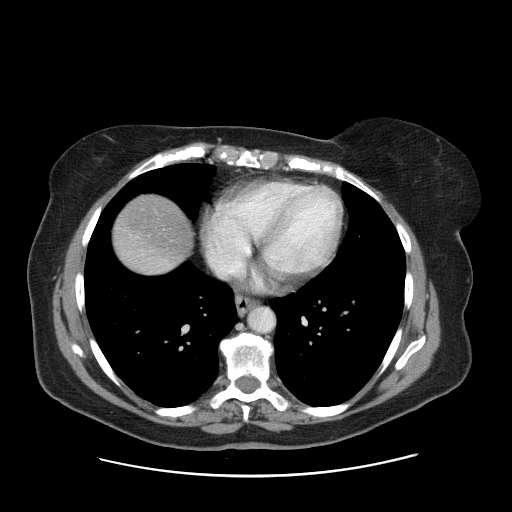
Contrast-enhanced abdominal CT, one axial slice; position 150 of 161 along the scan axis; soft-tissue window (W 400 / L 40 HU); 2.5 mm slice thickness; 512 × 512 image matrix, field of view 398 × 398 mm. Female patient, age 62 years. From the clinical record (not read from this slice): diagnosis: colorectal cancer liver metastases, imaged before liver resection; multiple liver metastases: no; largest metastasis: 2.5 cm; disease in both lobes: no.
Annotated regions visible in this slice (manually delineated by an expert):
- liver: bounding box [x1, y1, x2, y2] px = [114, 196, 191, 272]
- planned liver remnant (the part of the liver to remain after resection): [114, 196, 190, 267]